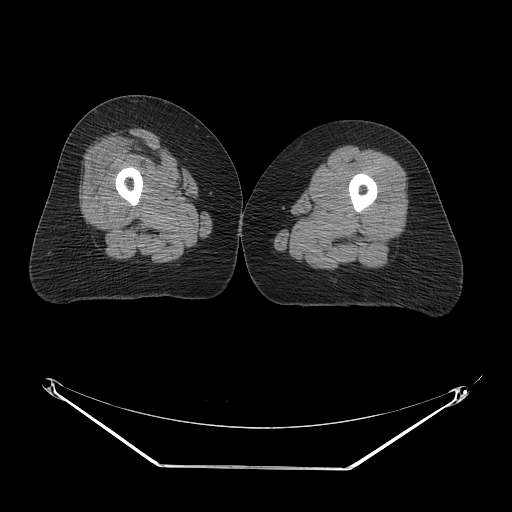
CT of an extremity soft-tissue mass (from a PET/CT study), one axial slice; position 18 of 267 along the scan axis; reconstruction kernel STANDARD; 140 kVp; soft-tissue window (W 400 / L 40 HU); 3.75 mm slice thickness; 512 × 512 image matrix, field of view 500 × 500 mm. Female patient. From the clinical record (not read from this slice): histological type: malignant solitary fibrous tumor; grade: intermediate; site of the primary tumour: right thigh.
Outlined on this slice (expert contour drawn on MRI and transferred to this co-registered scan by the dataset authors):
- gross tumour volume including surrounding oedema: bounding box <126,130,184,172> (left, top, right, bottom; pixels)